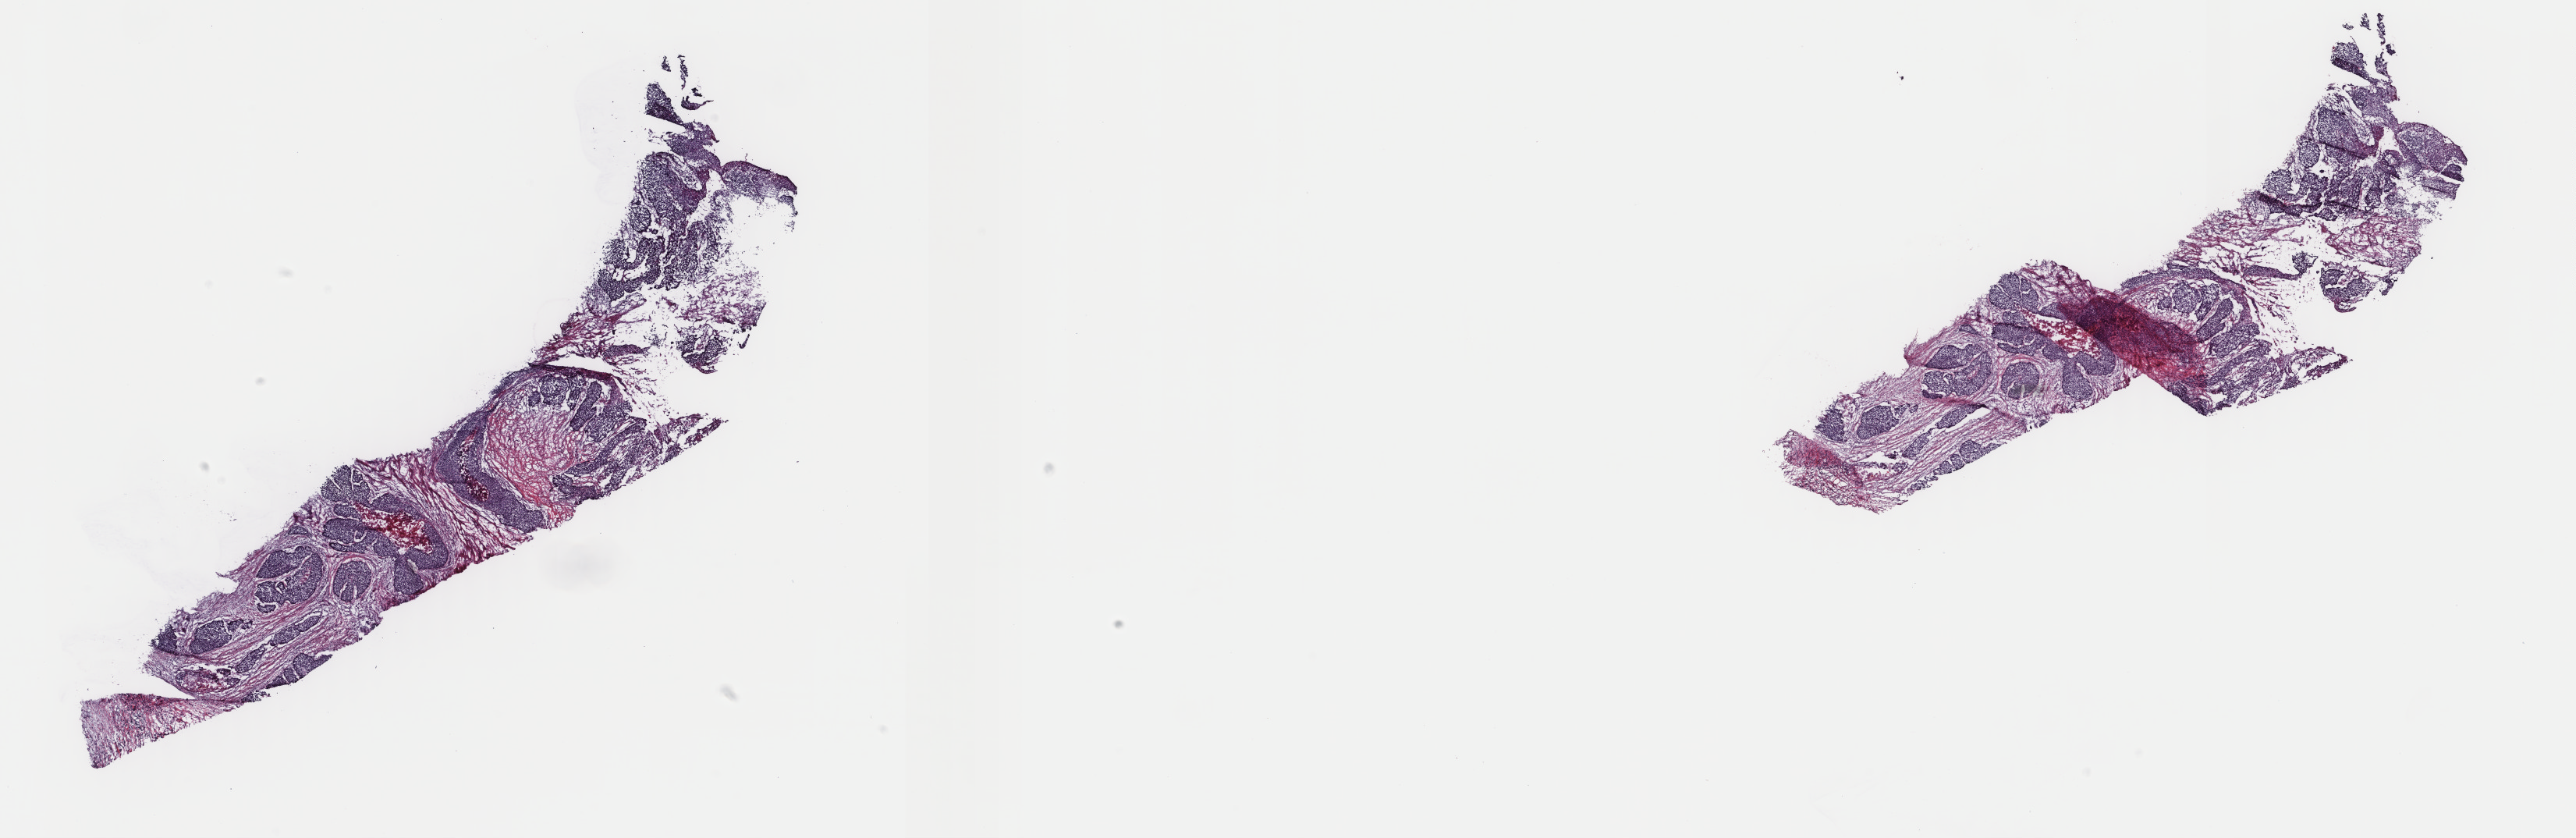
Whole-slide histology image, H&E-stained — shown as a low-resolution overview of the whole scanned area (about 26.2 x 8.5 mm), frozen section from the top of the tissue portion, esophagus, primary tumour sample. Female, age 51 years at initial diagnosis. Histologic grade: G2 (moderately differentiated). Composition of this section per pathologist review: tumour cells 55%, tumour nuclei 100%, normal cells 0%, stromal cells 40%, necrosis 5%. Infiltration values recorded for this section: lymphocyte infiltration 3%, monocyte infiltration 1%, neutrophil infiltration 0%.
* AJCC pathologic stage: IIA
* diagnosis: Squamous cell carcinoma, keratinizing, NOS
* lymph nodes positive (case pathology): 0 of 5 examined